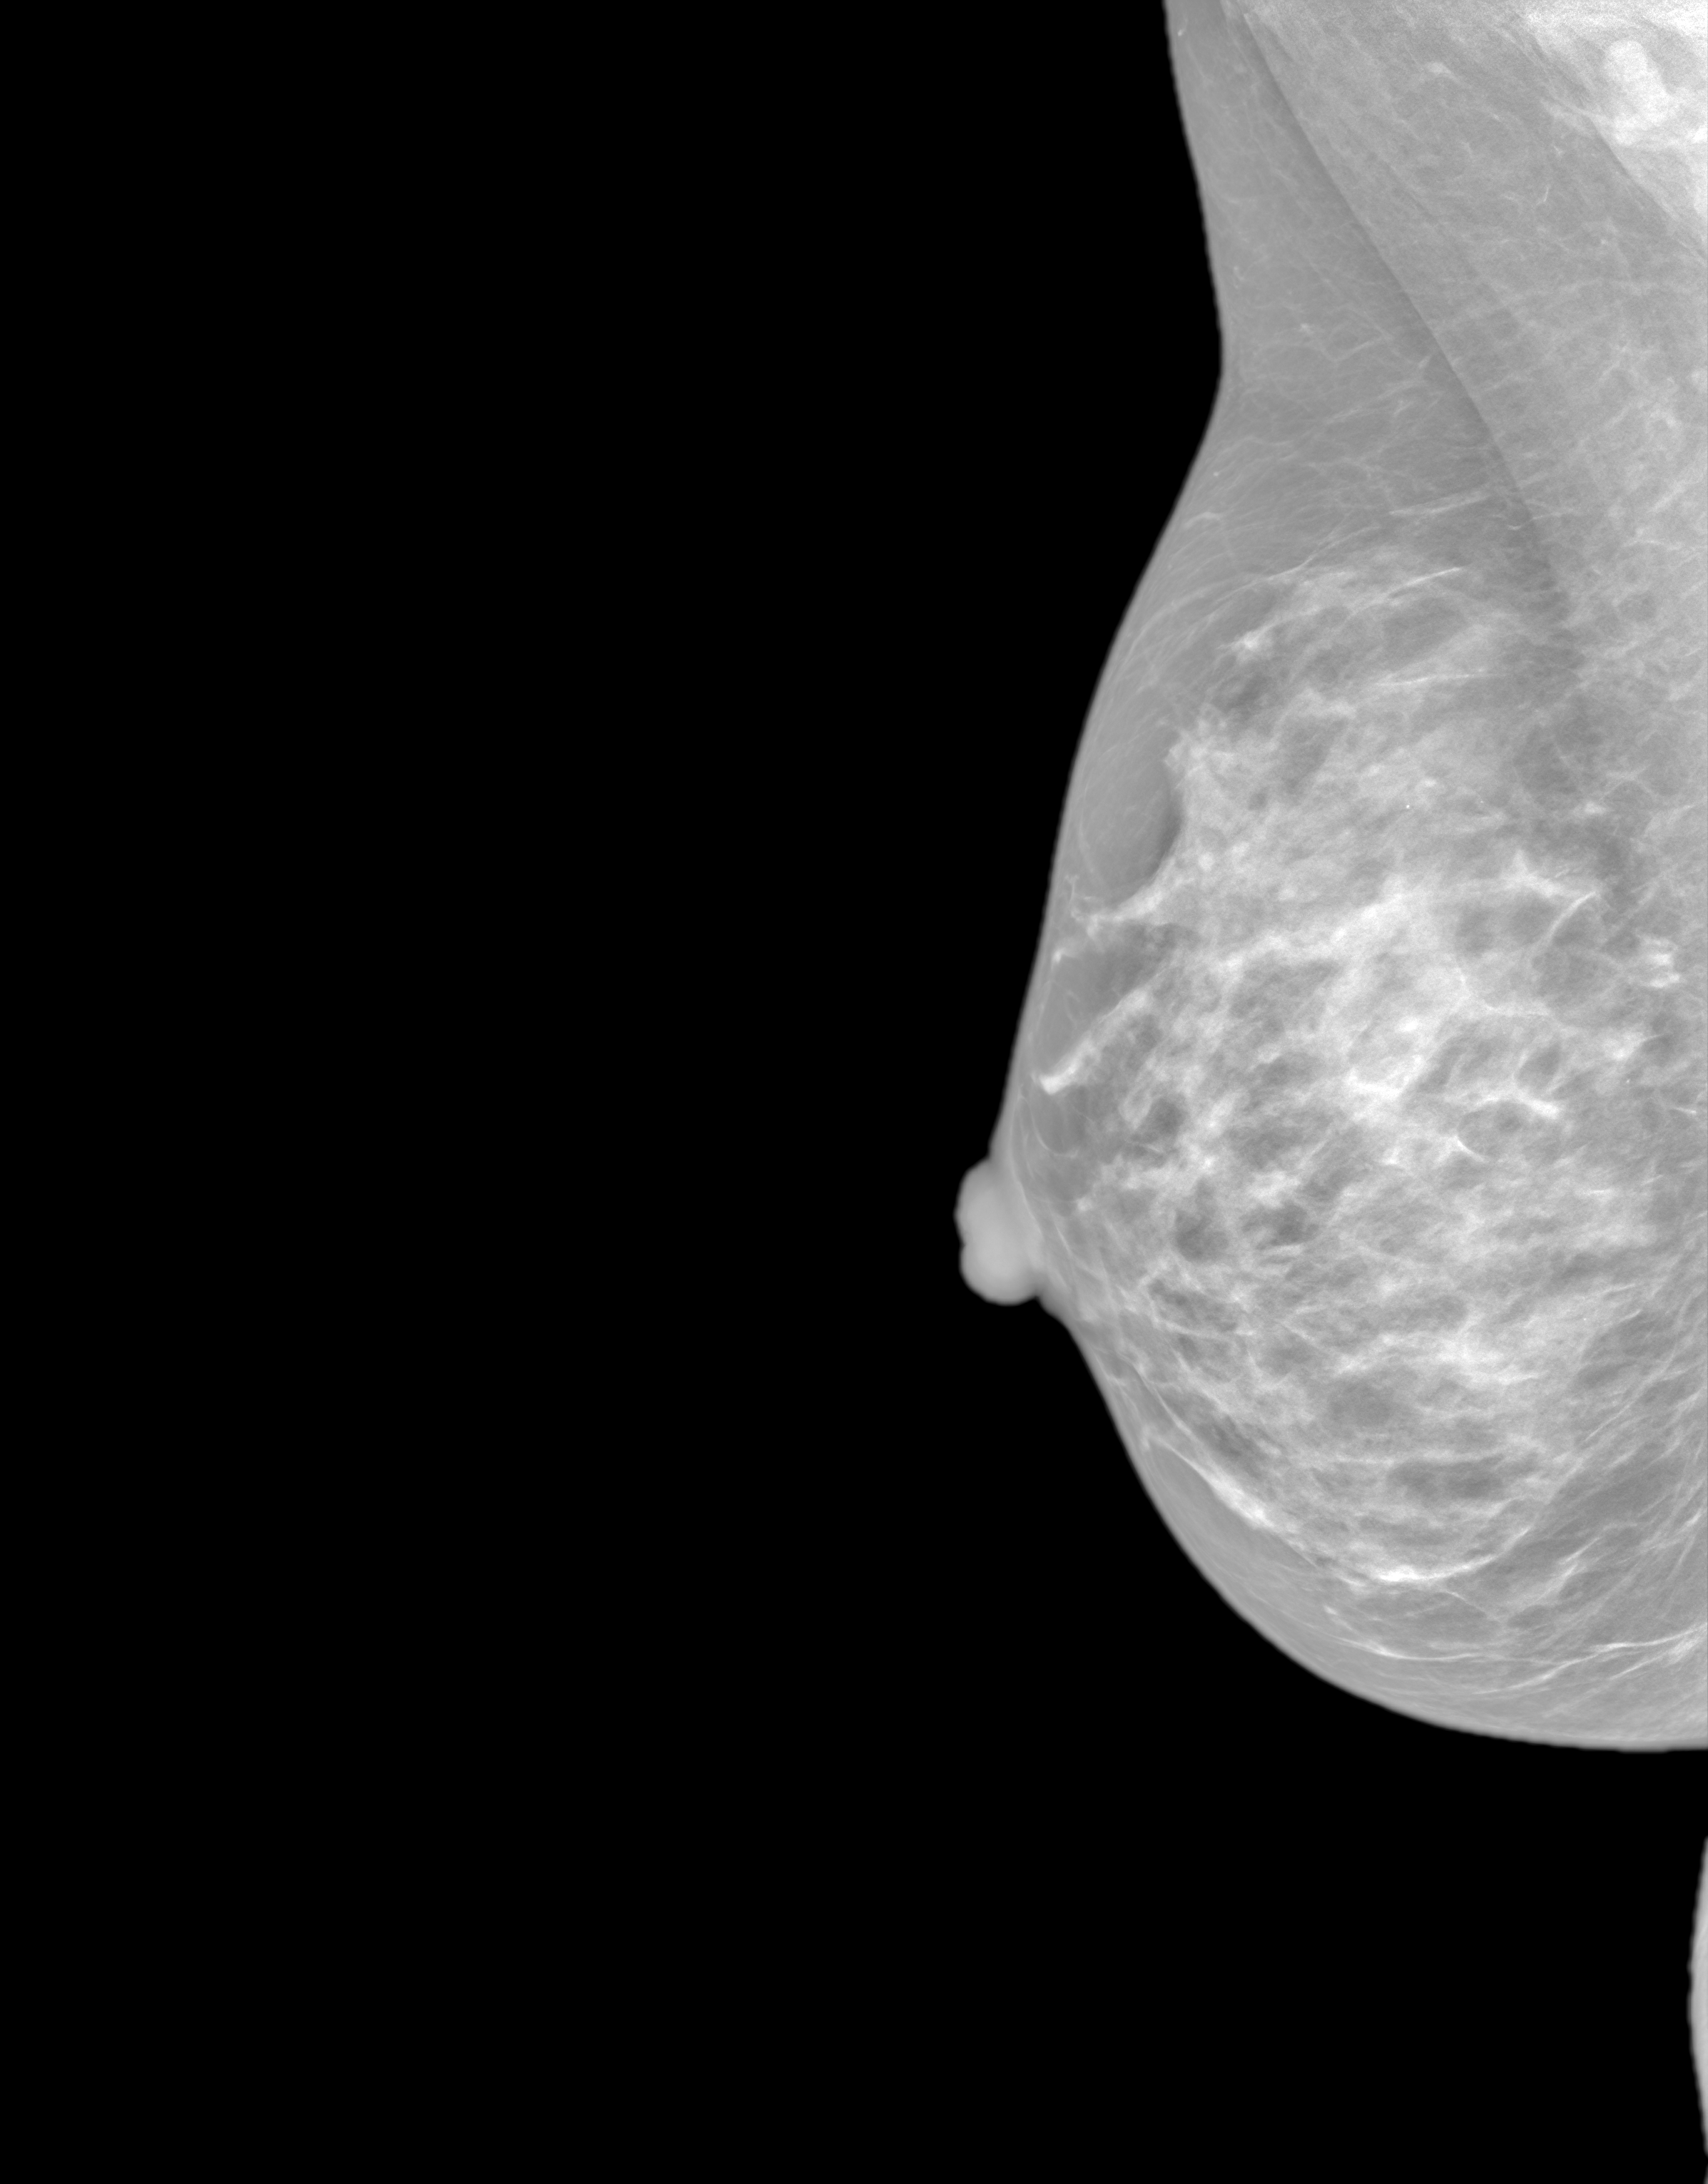
Synthesized 2-D mammogram reconstructed from digital breast tomosynthesis, right breast, medio-lateral oblique projection, annual screening mammography examination, system: SenoIris_1SP1.1(421). Female patient, age 42 years.
Breast density at the screening exam (both breasts): extremely dense (BI-RADS density category d). Final BI-RADS assessment for this screening round (tomosynthesis exam, both breasts): category 1. Recall: no recall after this screen.